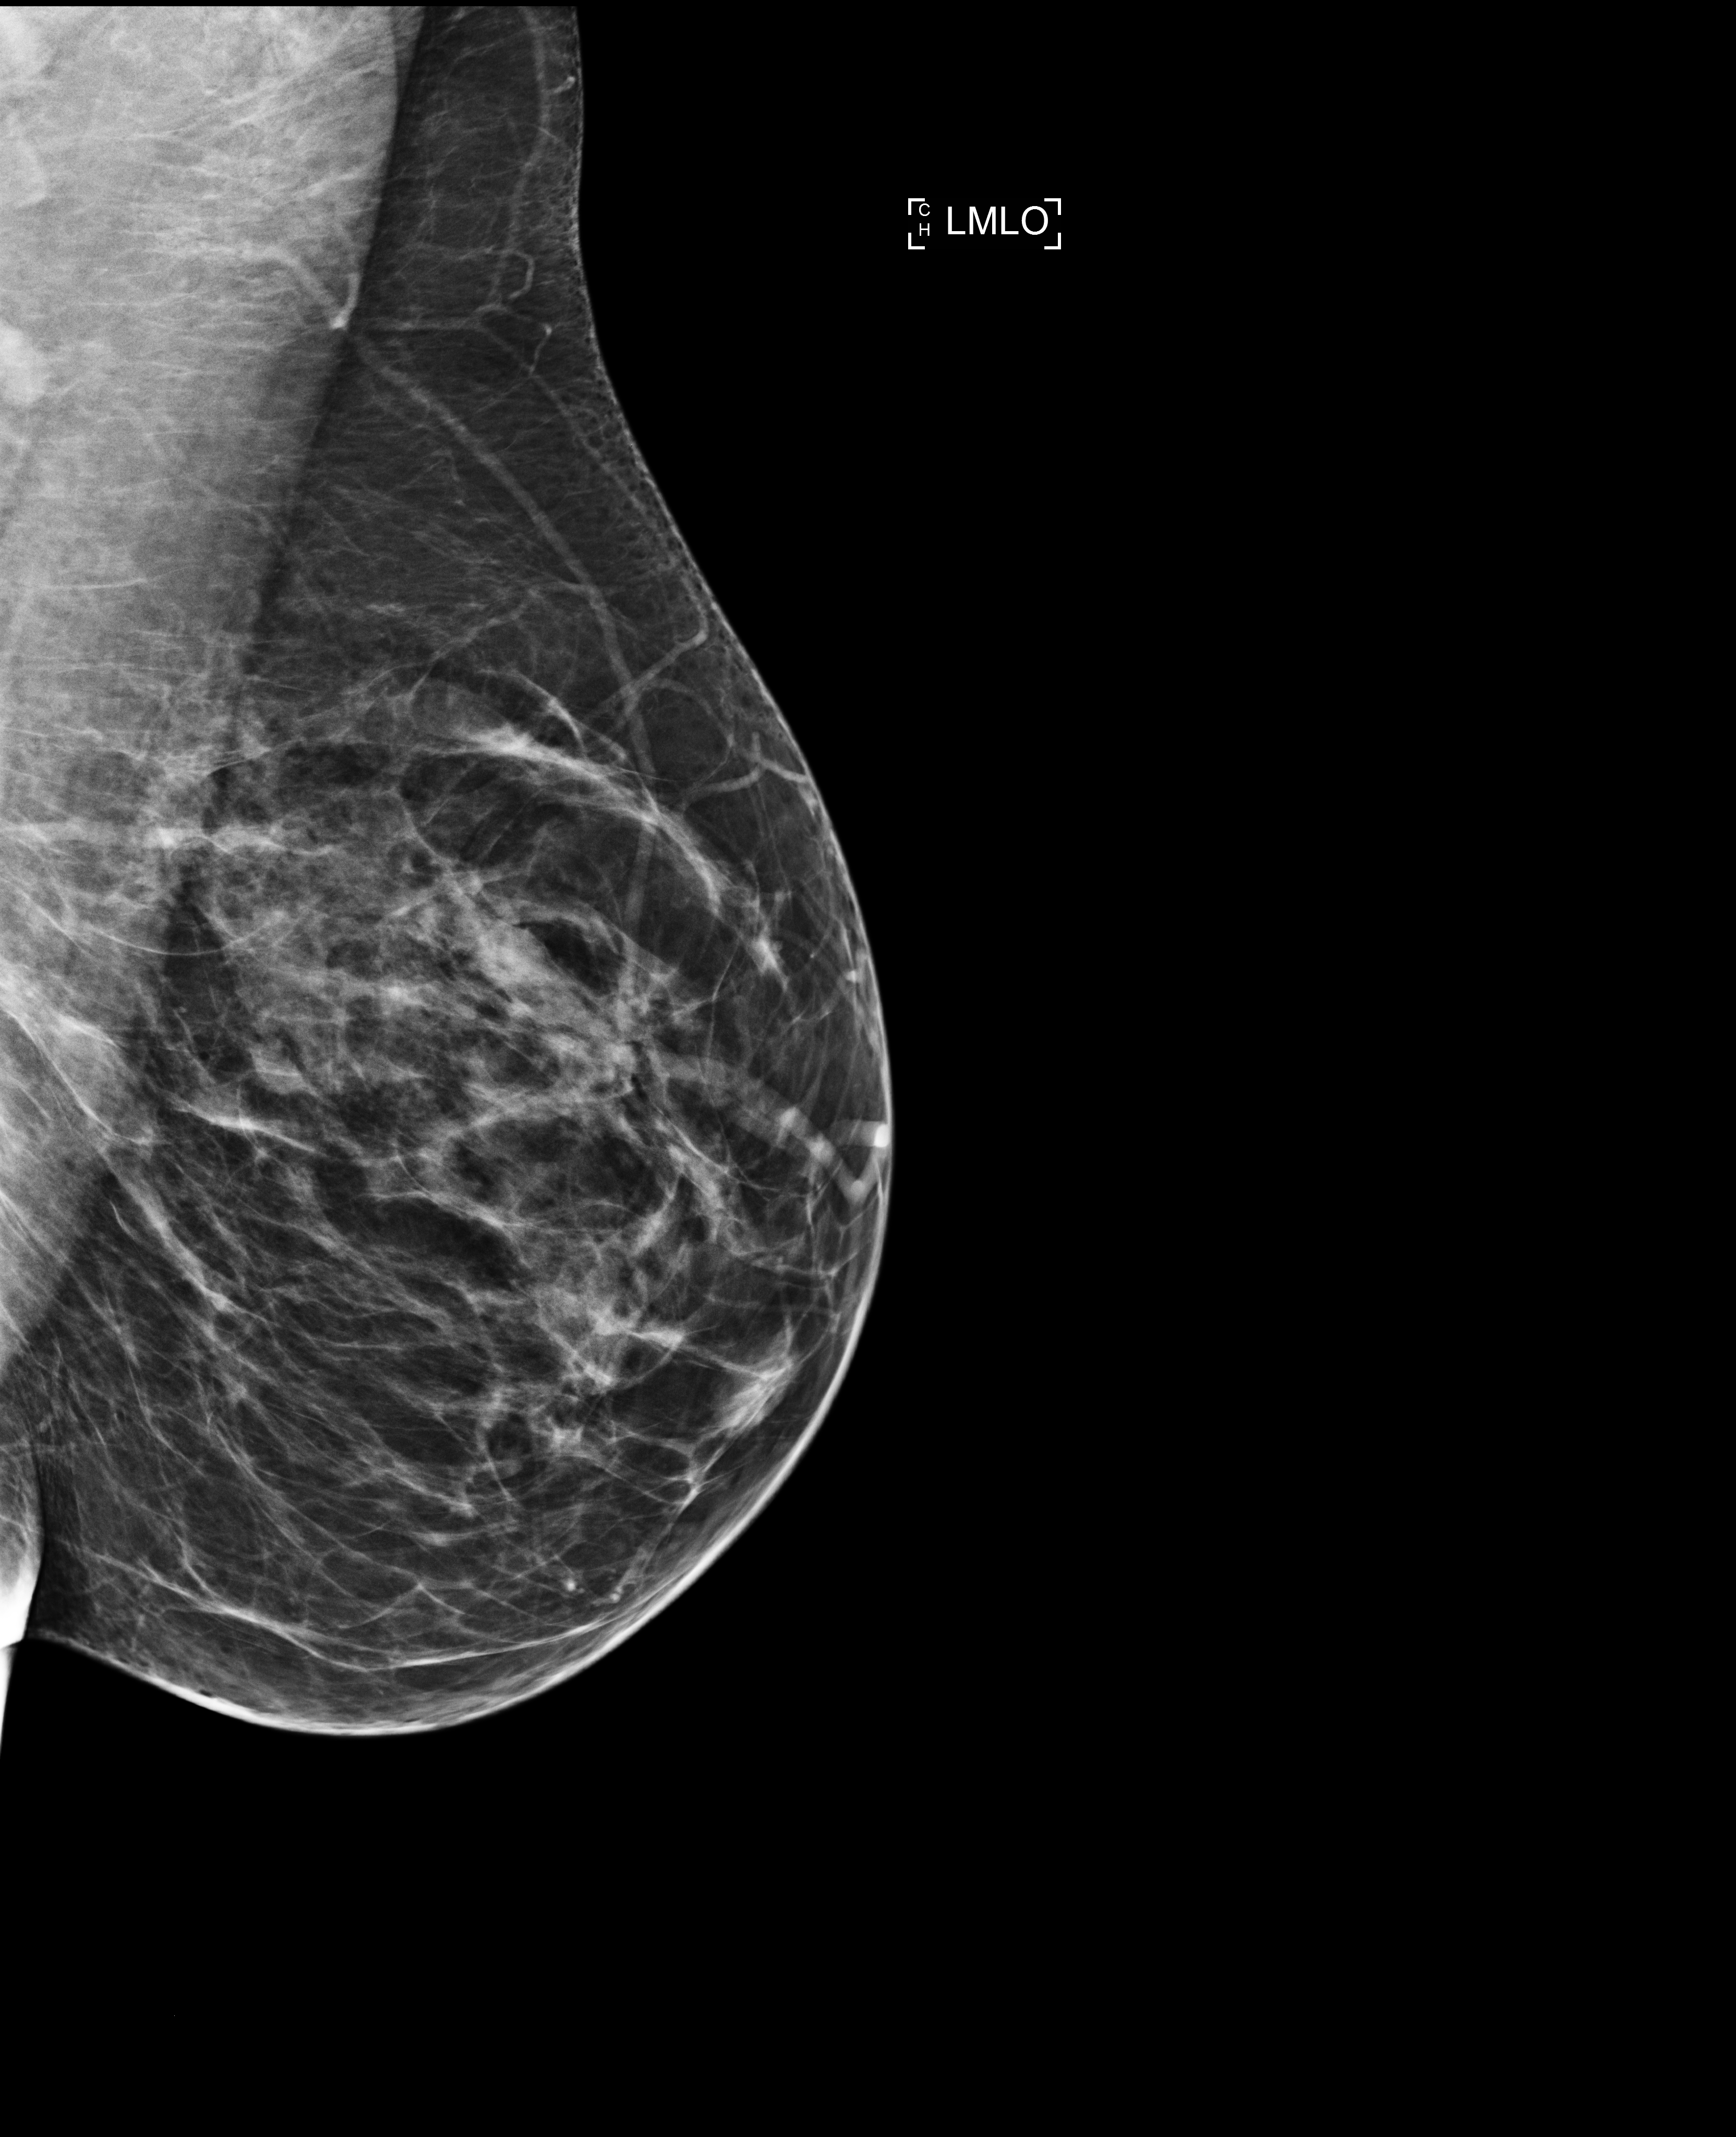
Full-field digital mammogram (FFDM), left breast, mediolateral oblique (MLO) view, annual screening mammography examination. Patient: female, 40 years.
BI-RADS breast density category at the screening exam (both breasts, scale 1–4): 2. Final BI-RADS assessment for this screening round (tomosynthesis exam, both breasts): category 1. Recall: no recall after this screen.